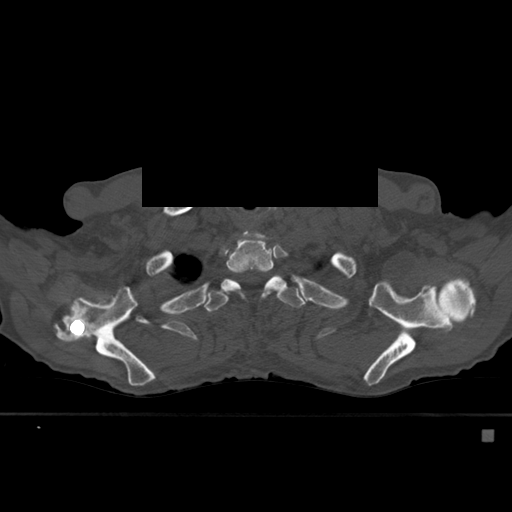
CT including the spine, one axial slice; slice 441 of 527 in the series (ordered by position); bone window (W 1800 / L 400 HU); 1.5 mm slice thickness; 512 × 512 image matrix, field of view 373 × 373 mm. Male patient, age 78 years. From the clinical record (not read from this slice): primary cancer: prostate.
Annotated regions visible in this slice (semi-automatic segmentation, software-assisted and operator-edited):
- T2 vertebra: bounding box (x1, y1, x2, y2) in pixels: (226, 232, 281, 298)
- T3 vertebra: (204, 271, 302, 312)